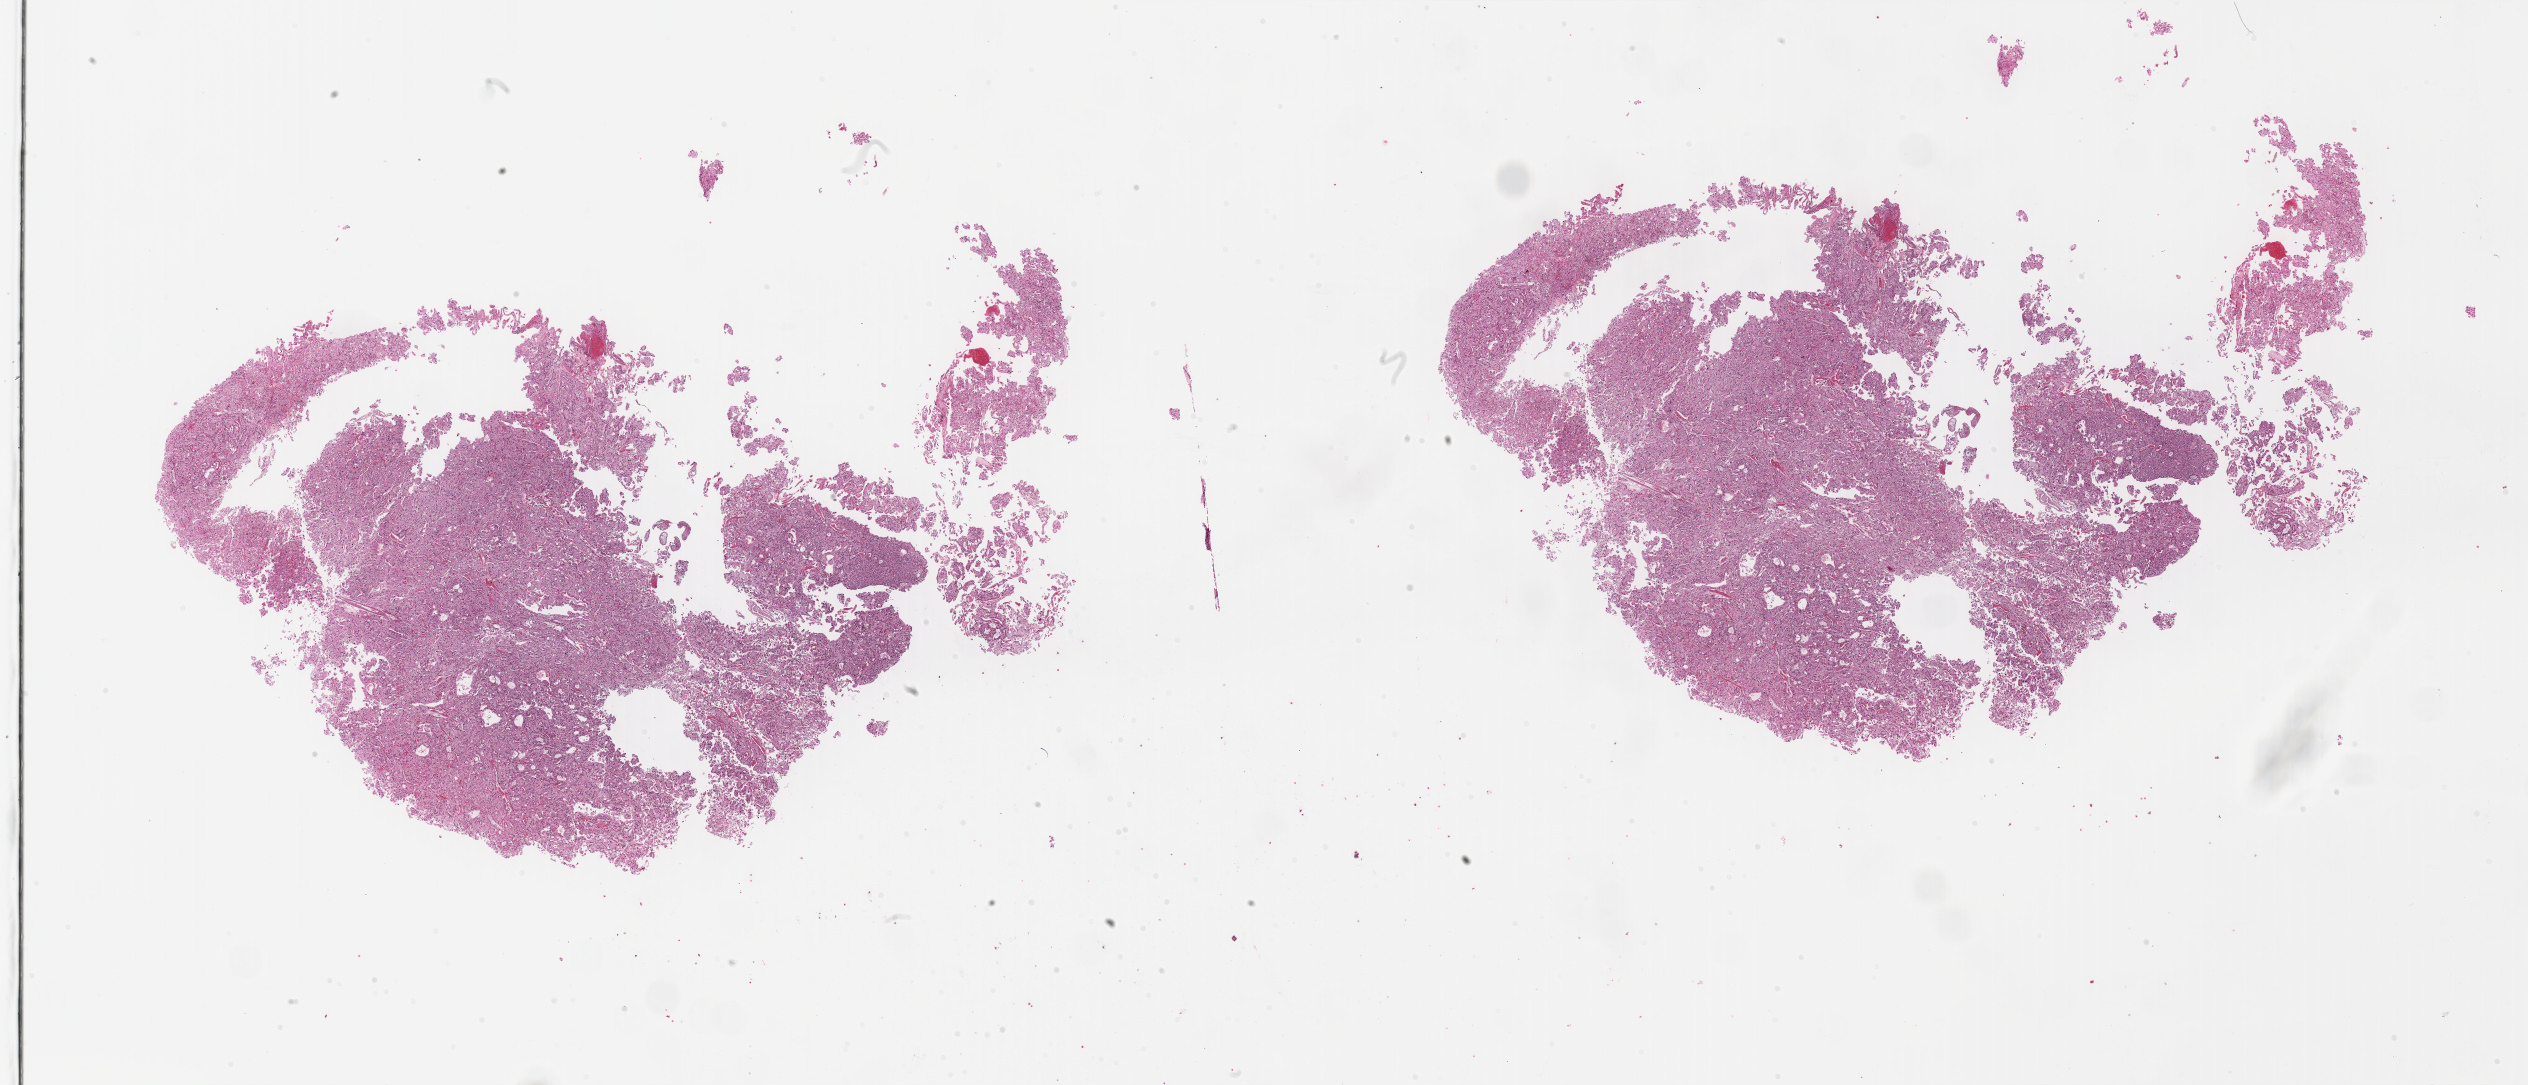
Digitized Hematoxylin and eosin (H&E) stained tissue section (whole slide) — a low-resolution overview of the entire scanned area, about 40.0 x 17.2 mm (from a 40x scan); formalin-fixed paraffin-embedded (FFPE) diagnostic section; primary tumour sample from the kidney. Male patient; age at initial diagnosis 57 years.
• laterality: right
• AJCC pathologic stage: III (7th edition)
• histologic diagnosis: Renal cell carcinoma, chromophobe type
• TNM: T3a NX